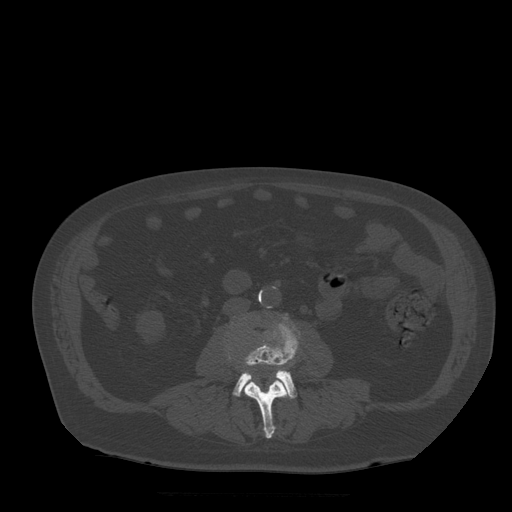
CT including the spine, one axial slice; position 130 of 522 along the scan axis; bone window (W 1800 / L 400 HU); 1.25 mm slice thickness; 512 × 512 image matrix. Patient age 72 years. Case-level facts recorded for this patient, not image findings: primary cancer: prostate.
Annotated regions visible in this slice (semi-automatically segmented with operator editing):
- L3 vertebra: bounding box <240,361,291,439> (left, top, right, bottom; pixels)
- L4 vertebra: <234,325,299,398>